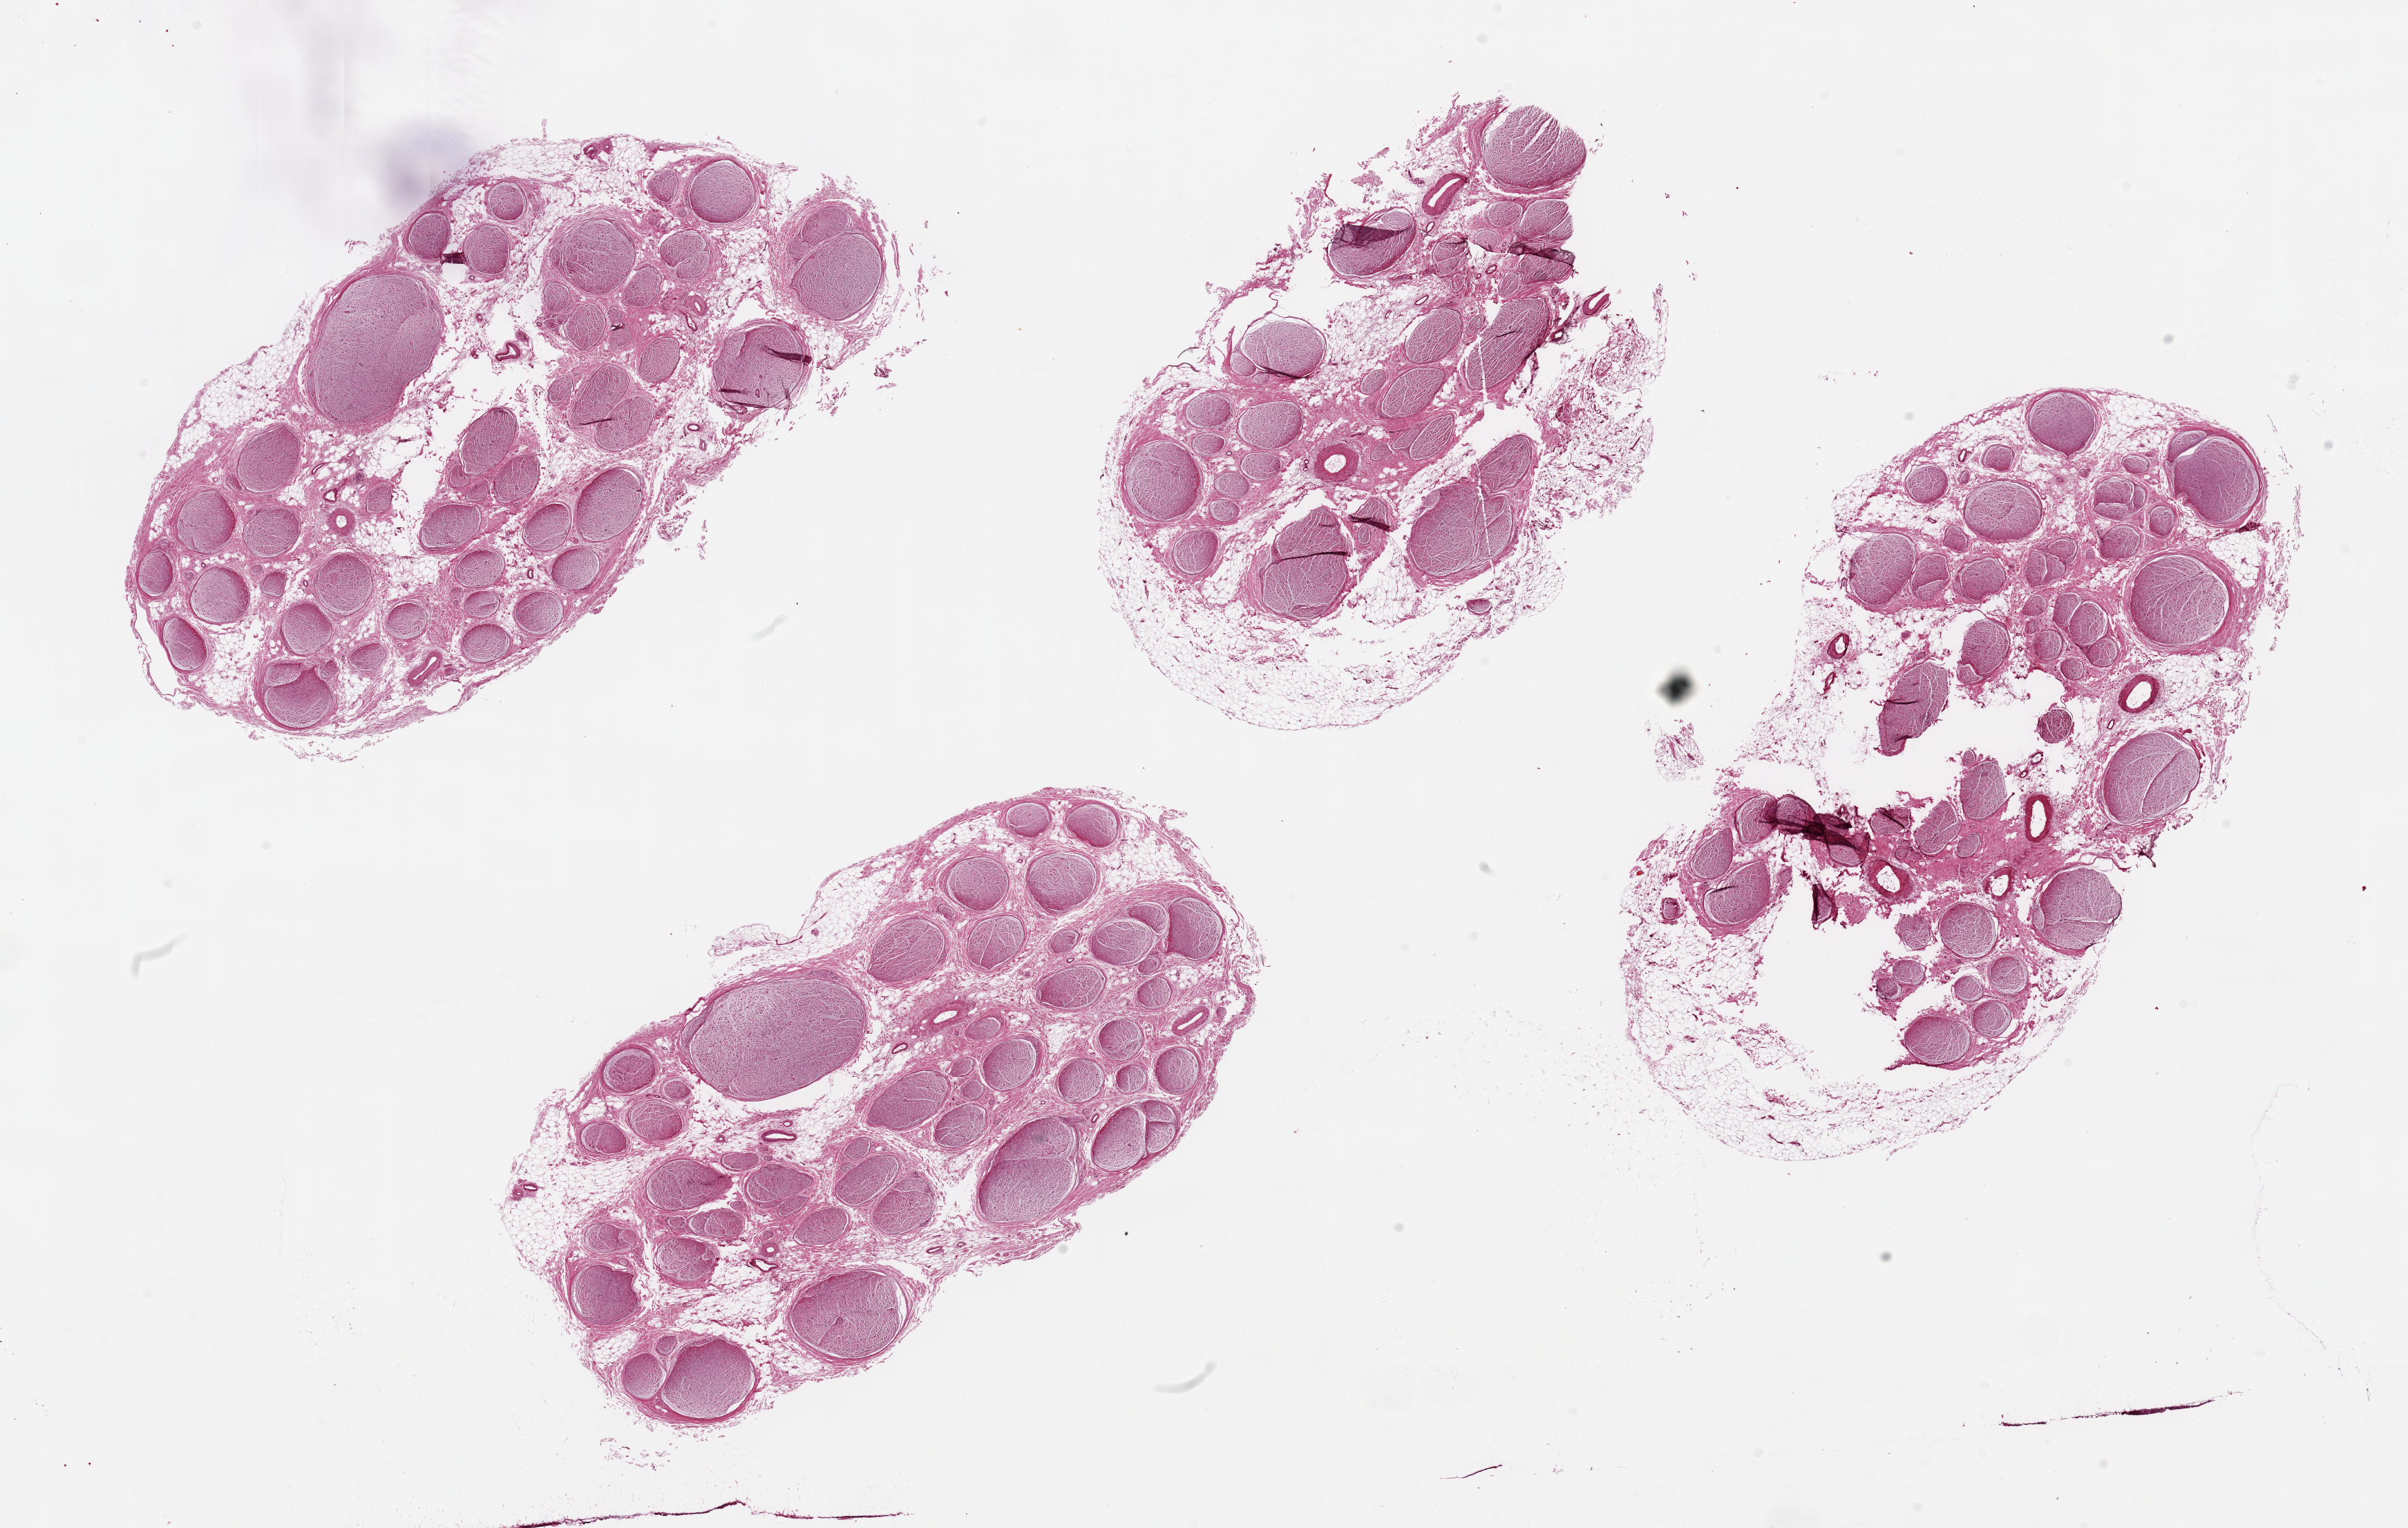
Haematoxylin and eosin whole-slide image, brightfield, a low-resolution overview of the entire scanned area, about 27.6 x 17.5 mm. PAXgene-fixed, paraffin-embedded tissue. Sampled site (target tissue): tibial nerve. Tissue donor sample. Donor sex: female.
- reviewer comment on this tissue sample: 4 pieces, up to 10x6mm; a few discontinous rims adherent fat up to ~0.5mm